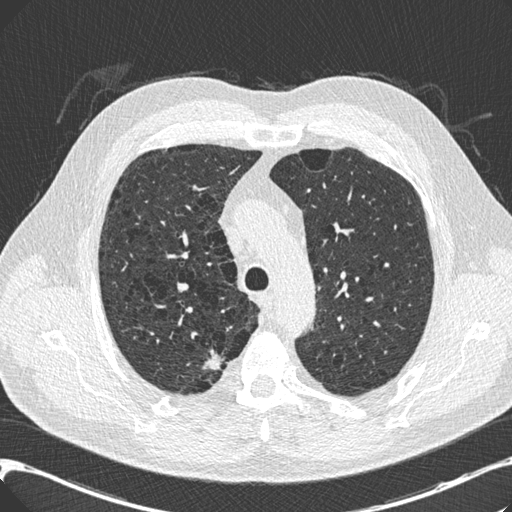
Low-dose screening chest CT, one axial slice; position 147 of 197 along the scan axis; reconstruction kernel B30f; 120 kVp; lung window (W 1500 / L -600 HU); 0.75 mm slice thickness; 512 × 512 image matrix, field of view 367 × 367 mm.
Outlined on this slice (expert manual segmentation):
- lesion 1 (tumor, upper lobe of right lung): bounding box [x1, y1, x2, y2] px = [202, 348, 222, 370]